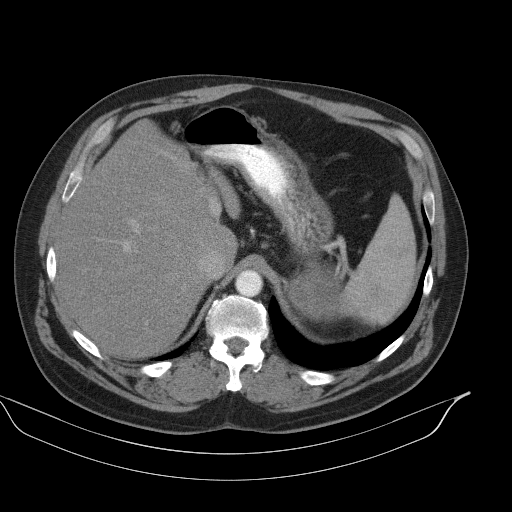
Contrast-enhanced abdominal CT, one axial slice; position 75 of 92 along the scan axis; intravenous contrast given; soft-tissue window (W 400 / L 40 HU); 512 × 512 image matrix. Patient: male, 56 years. Case-level facts recorded for this patient, not image findings: diagnosis: adrenocortical carcinoma; tumour side: left adrenal; tumour size at pathology: 15 cm; Ki-67 index: 35 %; stage (as recorded): 4.
Structures marked on this image (semi-automatic segmentation, software-assisted and operator-edited):
- mass: box from (x=292, y=263) to (x=340, y=320) px